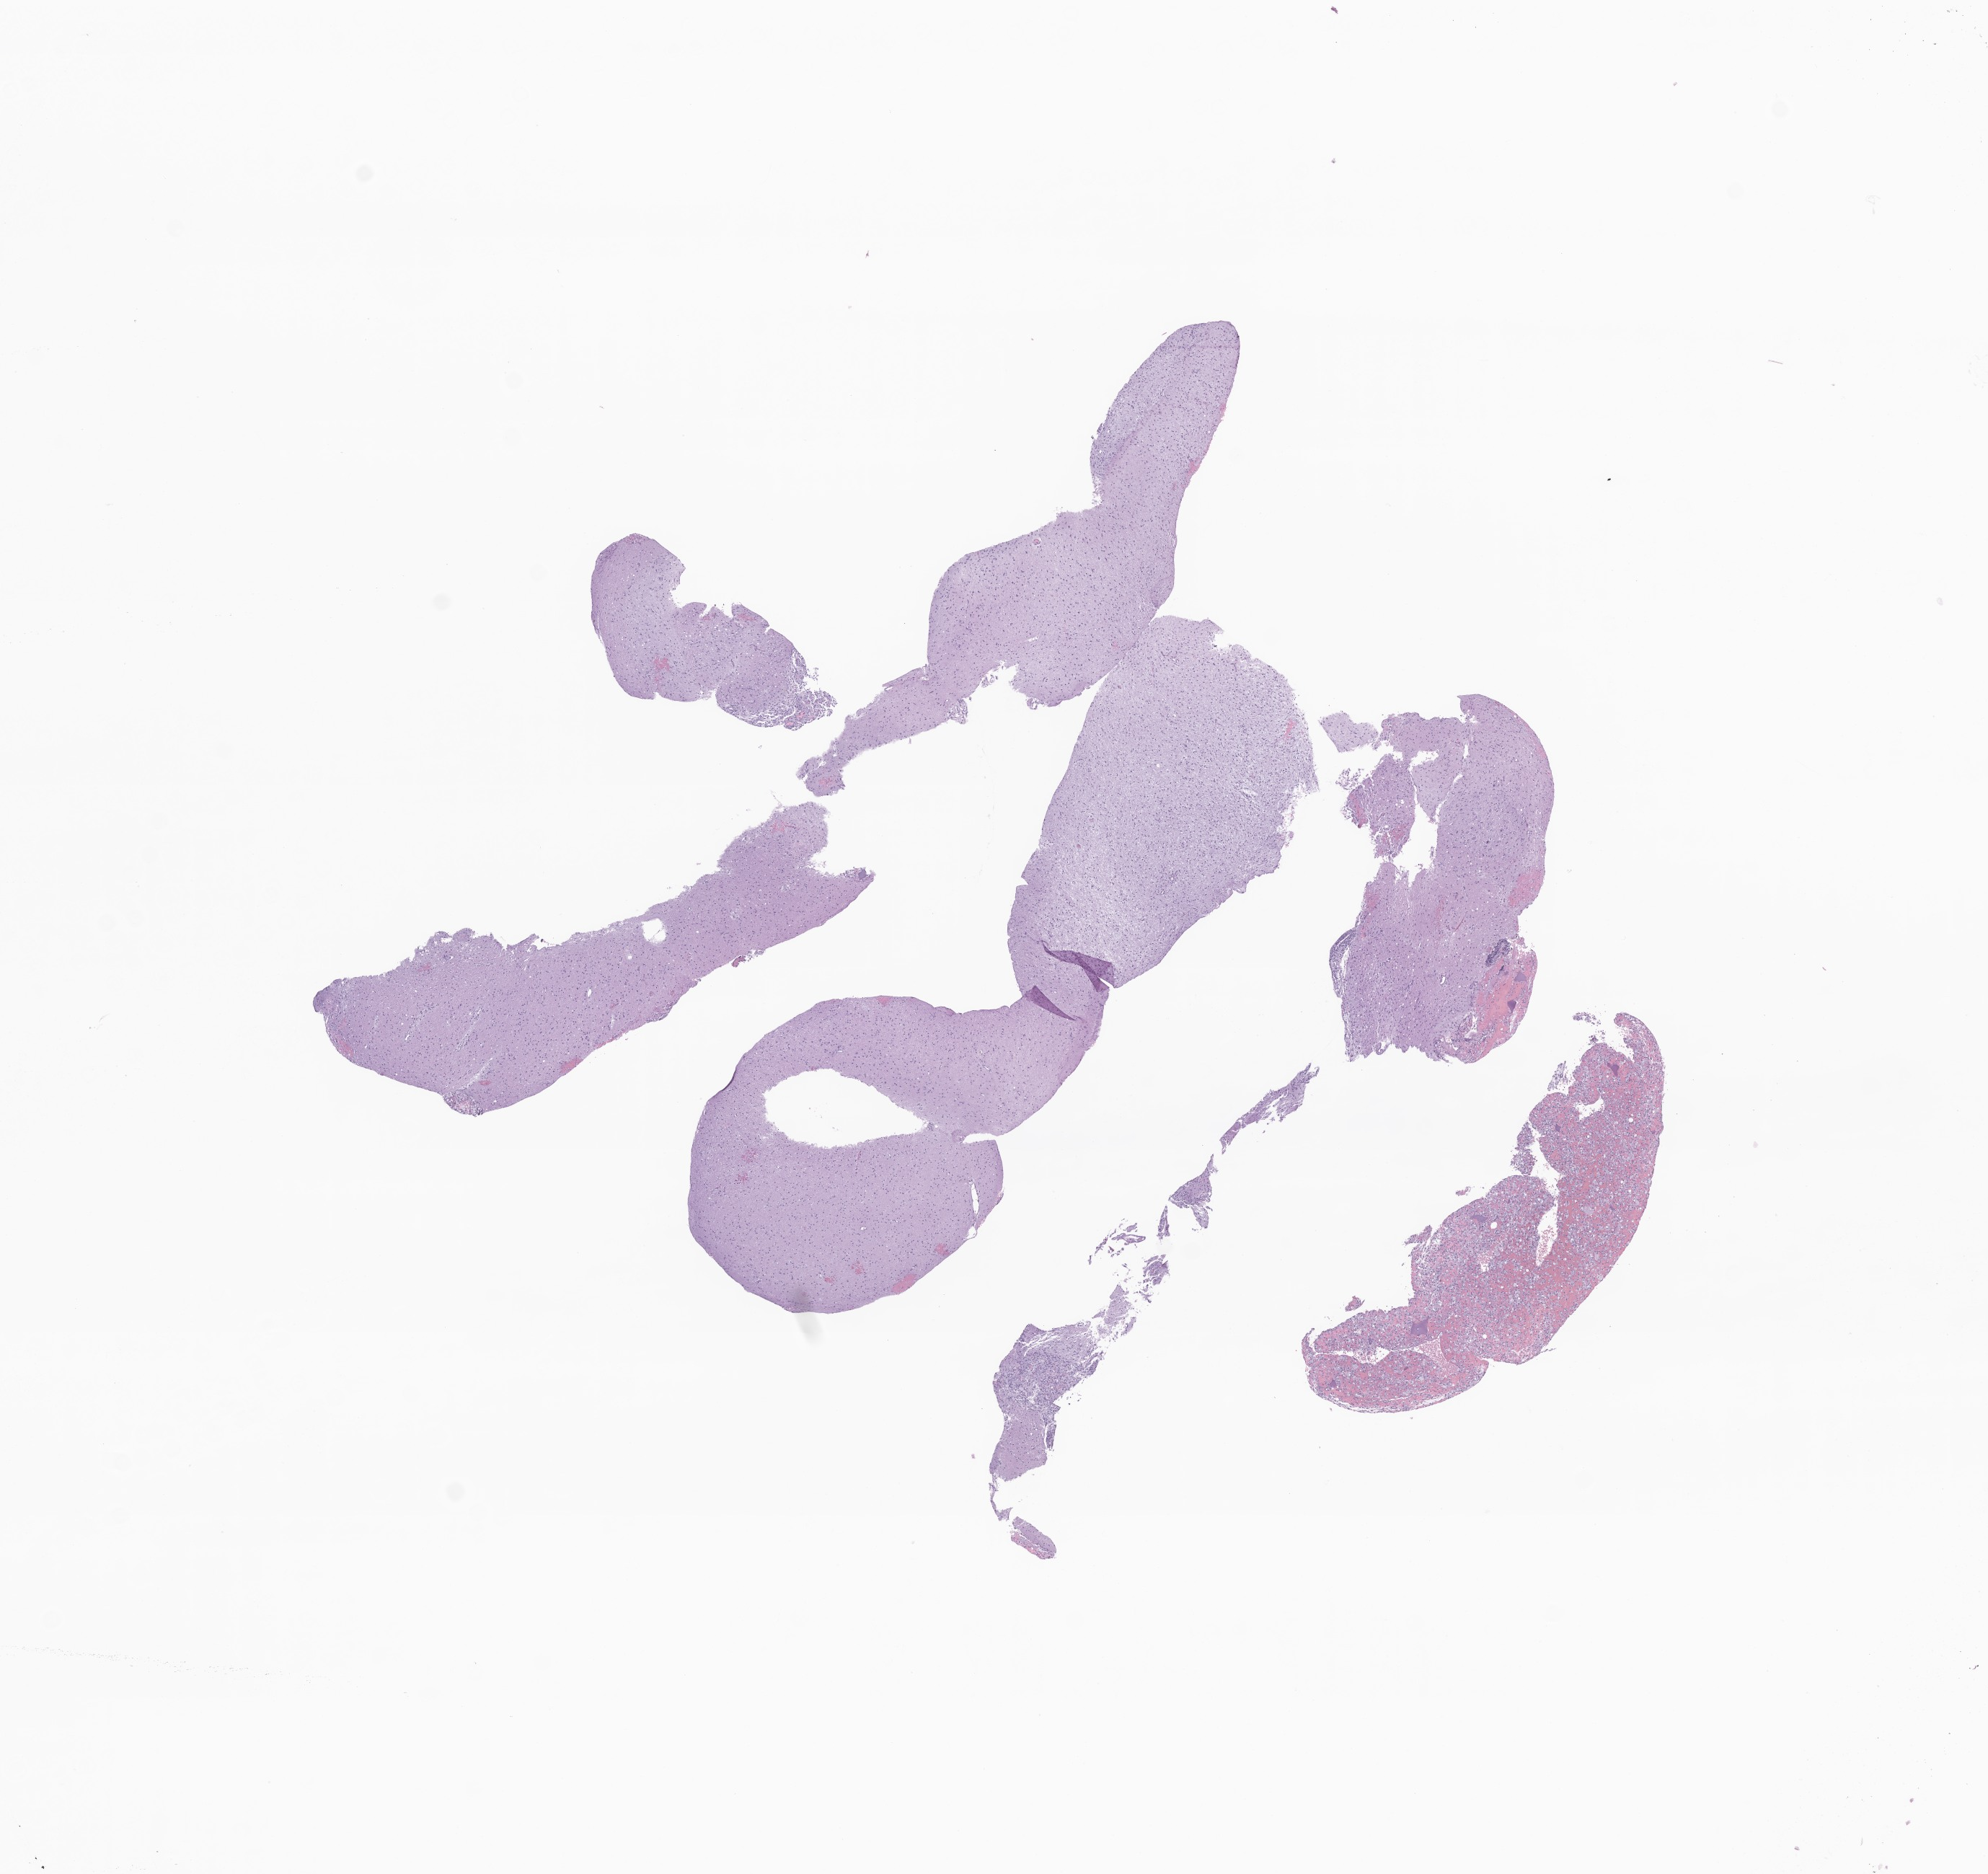
H&E whole-slide image of tumor tissue from the cerebellum — a low-resolution overview of the entire scanned area, about 11.6 x 11.0 mm. FFPE section. Male patient, age 63 months (5 years 3 months).
Recorded diagnosis: Neoplasm, uncertain whether benign or malignant.